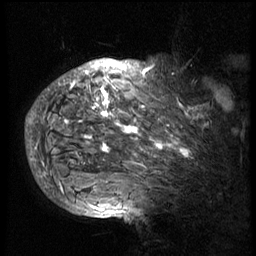
Breast MRI (dynamic contrast-enhanced), one sagittal slice; slice 58 of 74 in the series (ordered by position); 3 images stored at this slice position (order not interpretable as contrast timing); 1.5 T; TE 4.2 ms, TR 8.9 ms; 2.5 mm slice thickness; 256 × 256 image matrix, field of view 200 × 200 mm. Patient: female, 57 years. Case-level facts recorded for this patient, not image findings: setting: breast cancer imaged before/during neoadjuvant chemotherapy; receptor status: HER2-positive.
Annotated regions visible in this slice (semi-automatically segmented with operator editing):
- analysis volume of interest (the breast-tissue region the enhancement analysis was run in; not a lesion): bounding box [x1, y1, x2, y2] px = [40, 62, 240, 175]
- tumour enhancement mask (voxels above the 140 % enhancement threshold inside the analysis volume of interest): [40, 64, 203, 175]